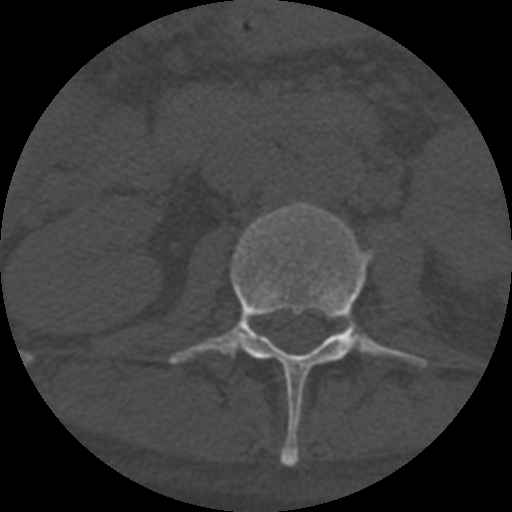
CT including the spine, one axial slice. Position 259 of 708 along the scan axis. 120 kVp. One of 3 acquisitions stored at this slice position. Bone window (W 1800 / L 400 HU). 1.25 mm slice thickness. 512 × 512 image matrix, field of view 160 × 160 mm. Patient age 55 years. Case-level facts recorded for this patient, not image findings: primary cancer: colon; vertebrae with lytic lesions (as recorded): T12, L1, L5.
Annotated regions visible in this slice (semi-automatic segmentation, software-assisted and operator-edited):
- L2 vertebra: bounding box [x1, y1, x2, y2] px = [168, 203, 428, 466]